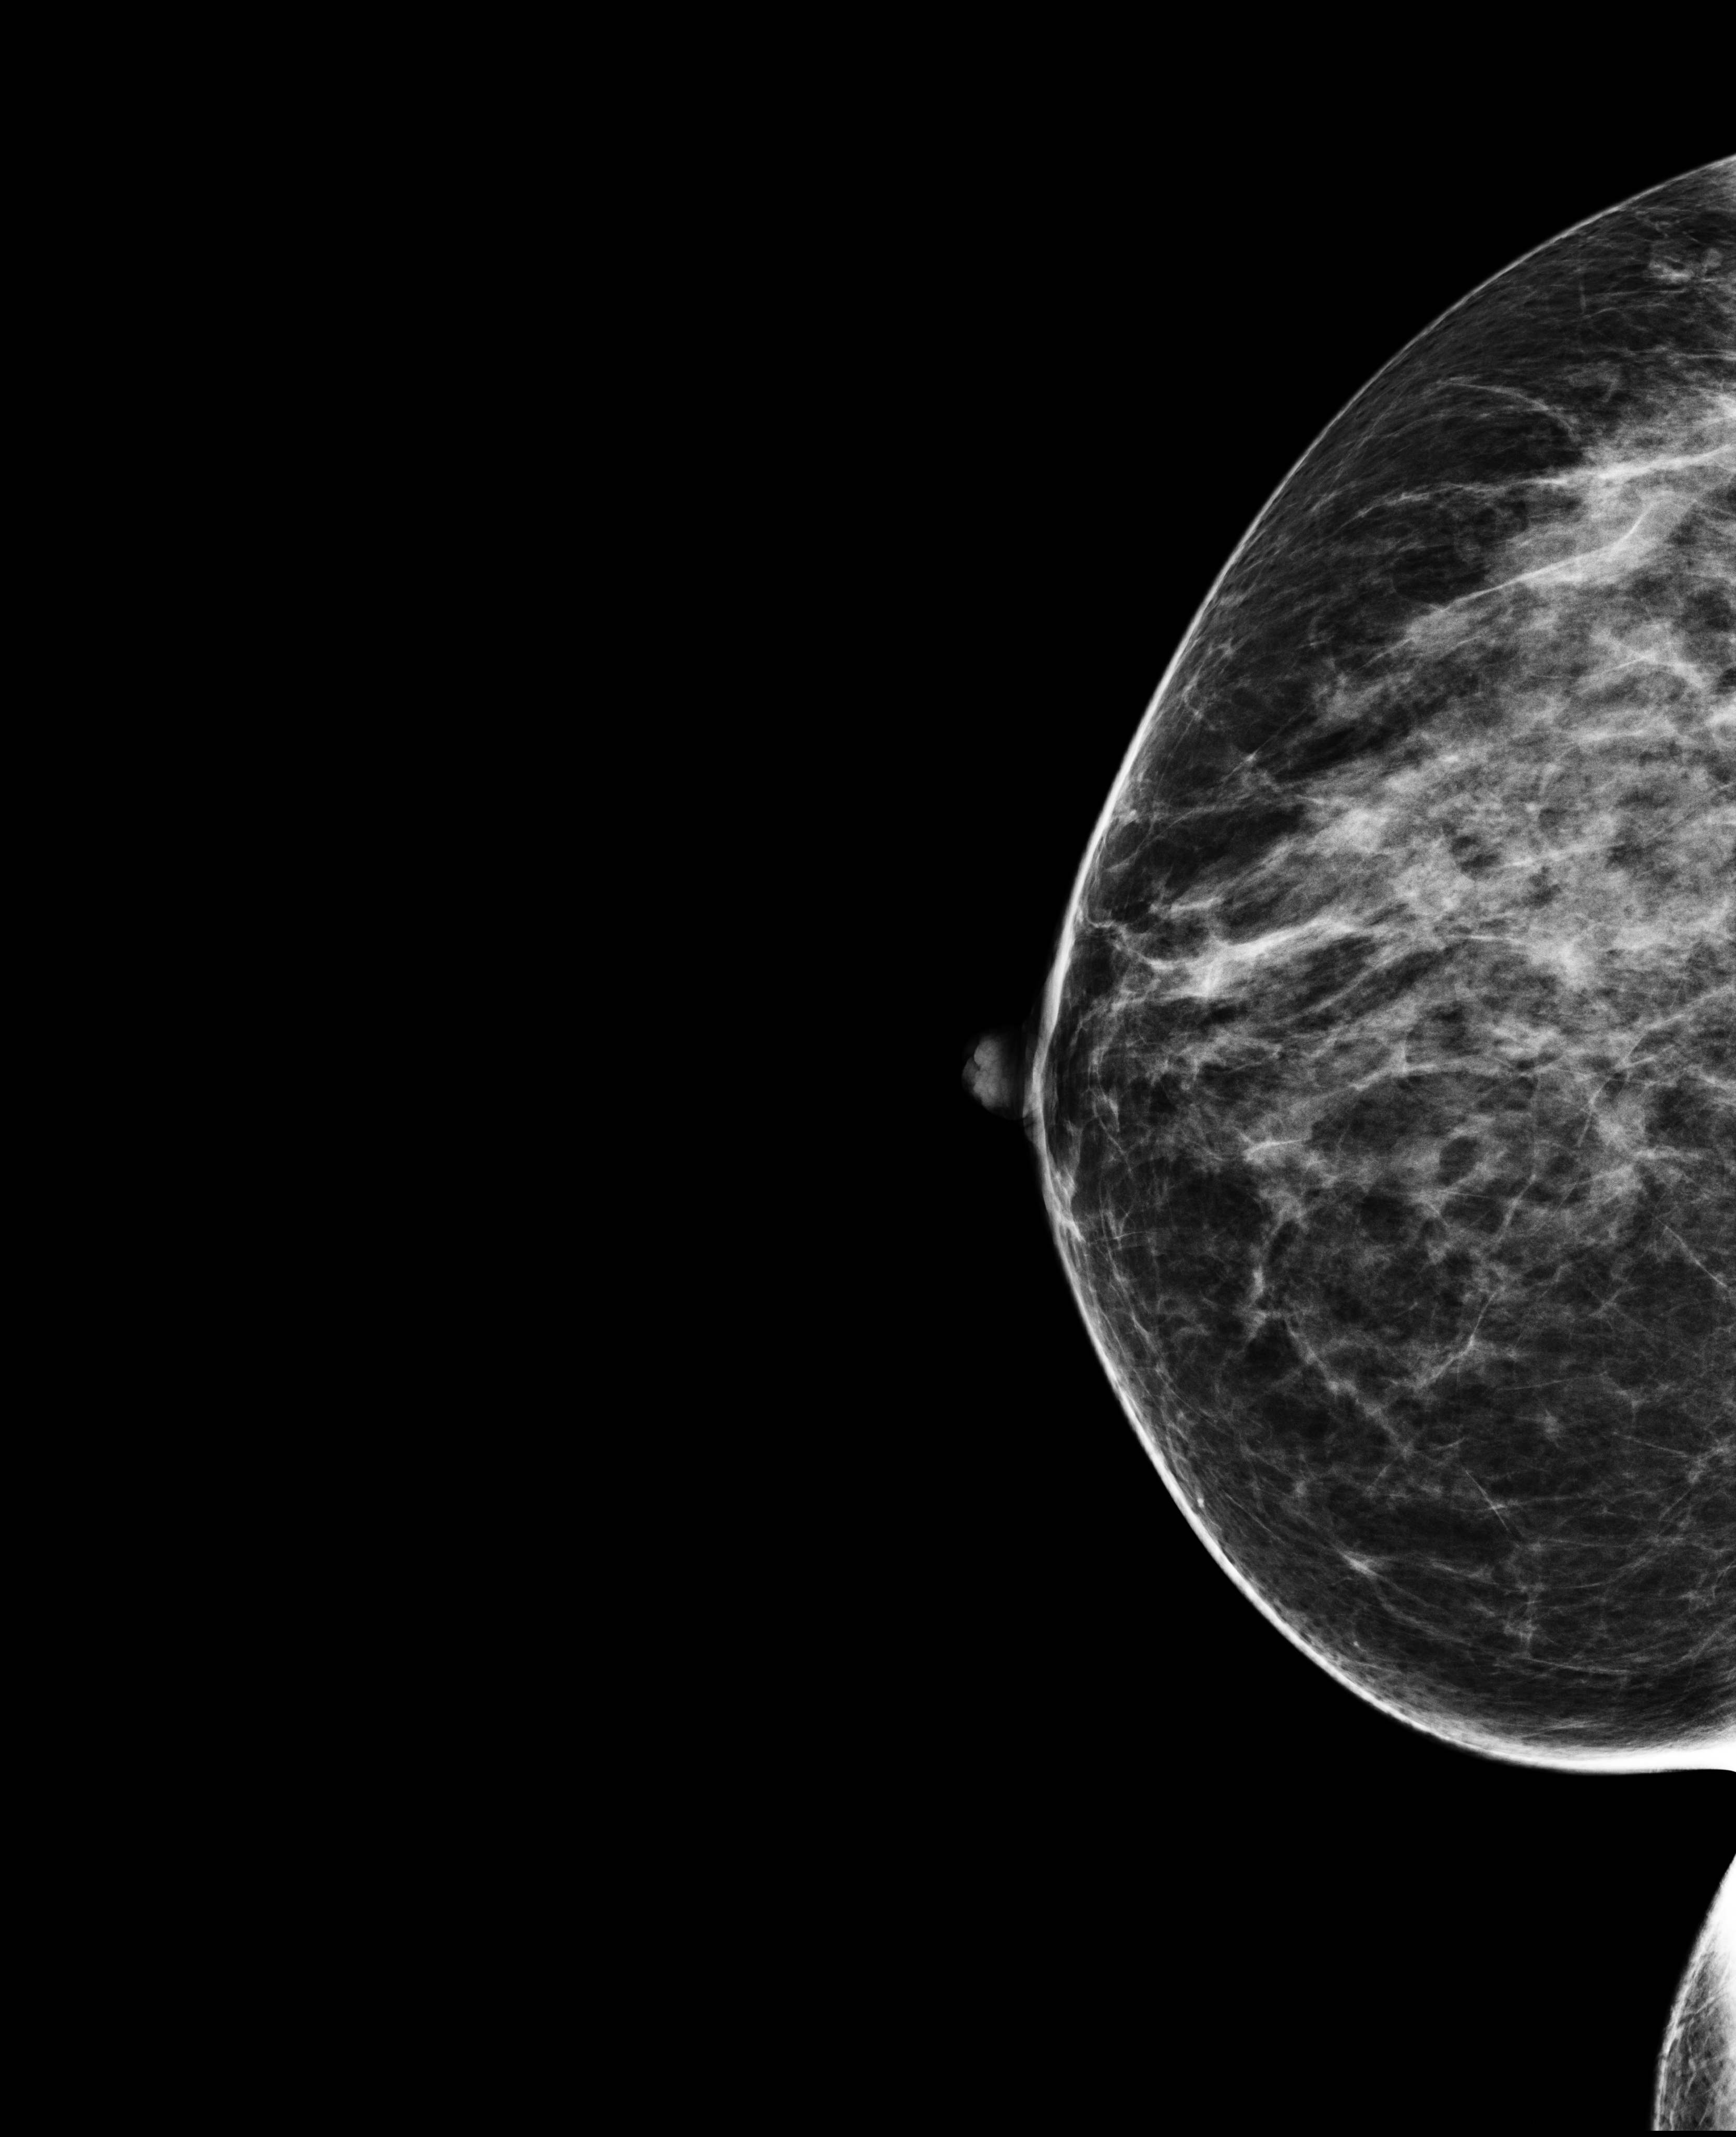
Screening examination. Patient aged 45 years (female).
Image type: full-field digital mammogram. Breast: right. Projection: CC view.